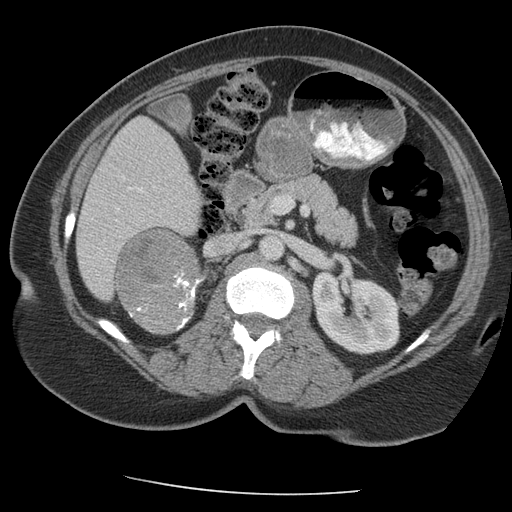
Contrast-enhanced abdominal CT, one axial slice; position 114 of 163 along the scan axis; reconstruction kernel STANDARD; intravenous contrast given; soft-tissue window (W 400 / L 40 HU); 2.5 mm slice thickness; 512 × 512 image matrix, field of view 360 × 360 mm. Female patient, age 70 years. From the clinical record (not read from this slice): diagnosis: adrenocortical carcinoma; tumour side: right adrenal; tumour size at pathology: 9.5 cm; Ki-67 index: 5 %; stage (as recorded): 2.
Outlined on this slice (semi-automatic segmentation, software-assisted and operator-edited):
- mass: bounding box [x1, y1, x2, y2] px = [117, 229, 199, 334]